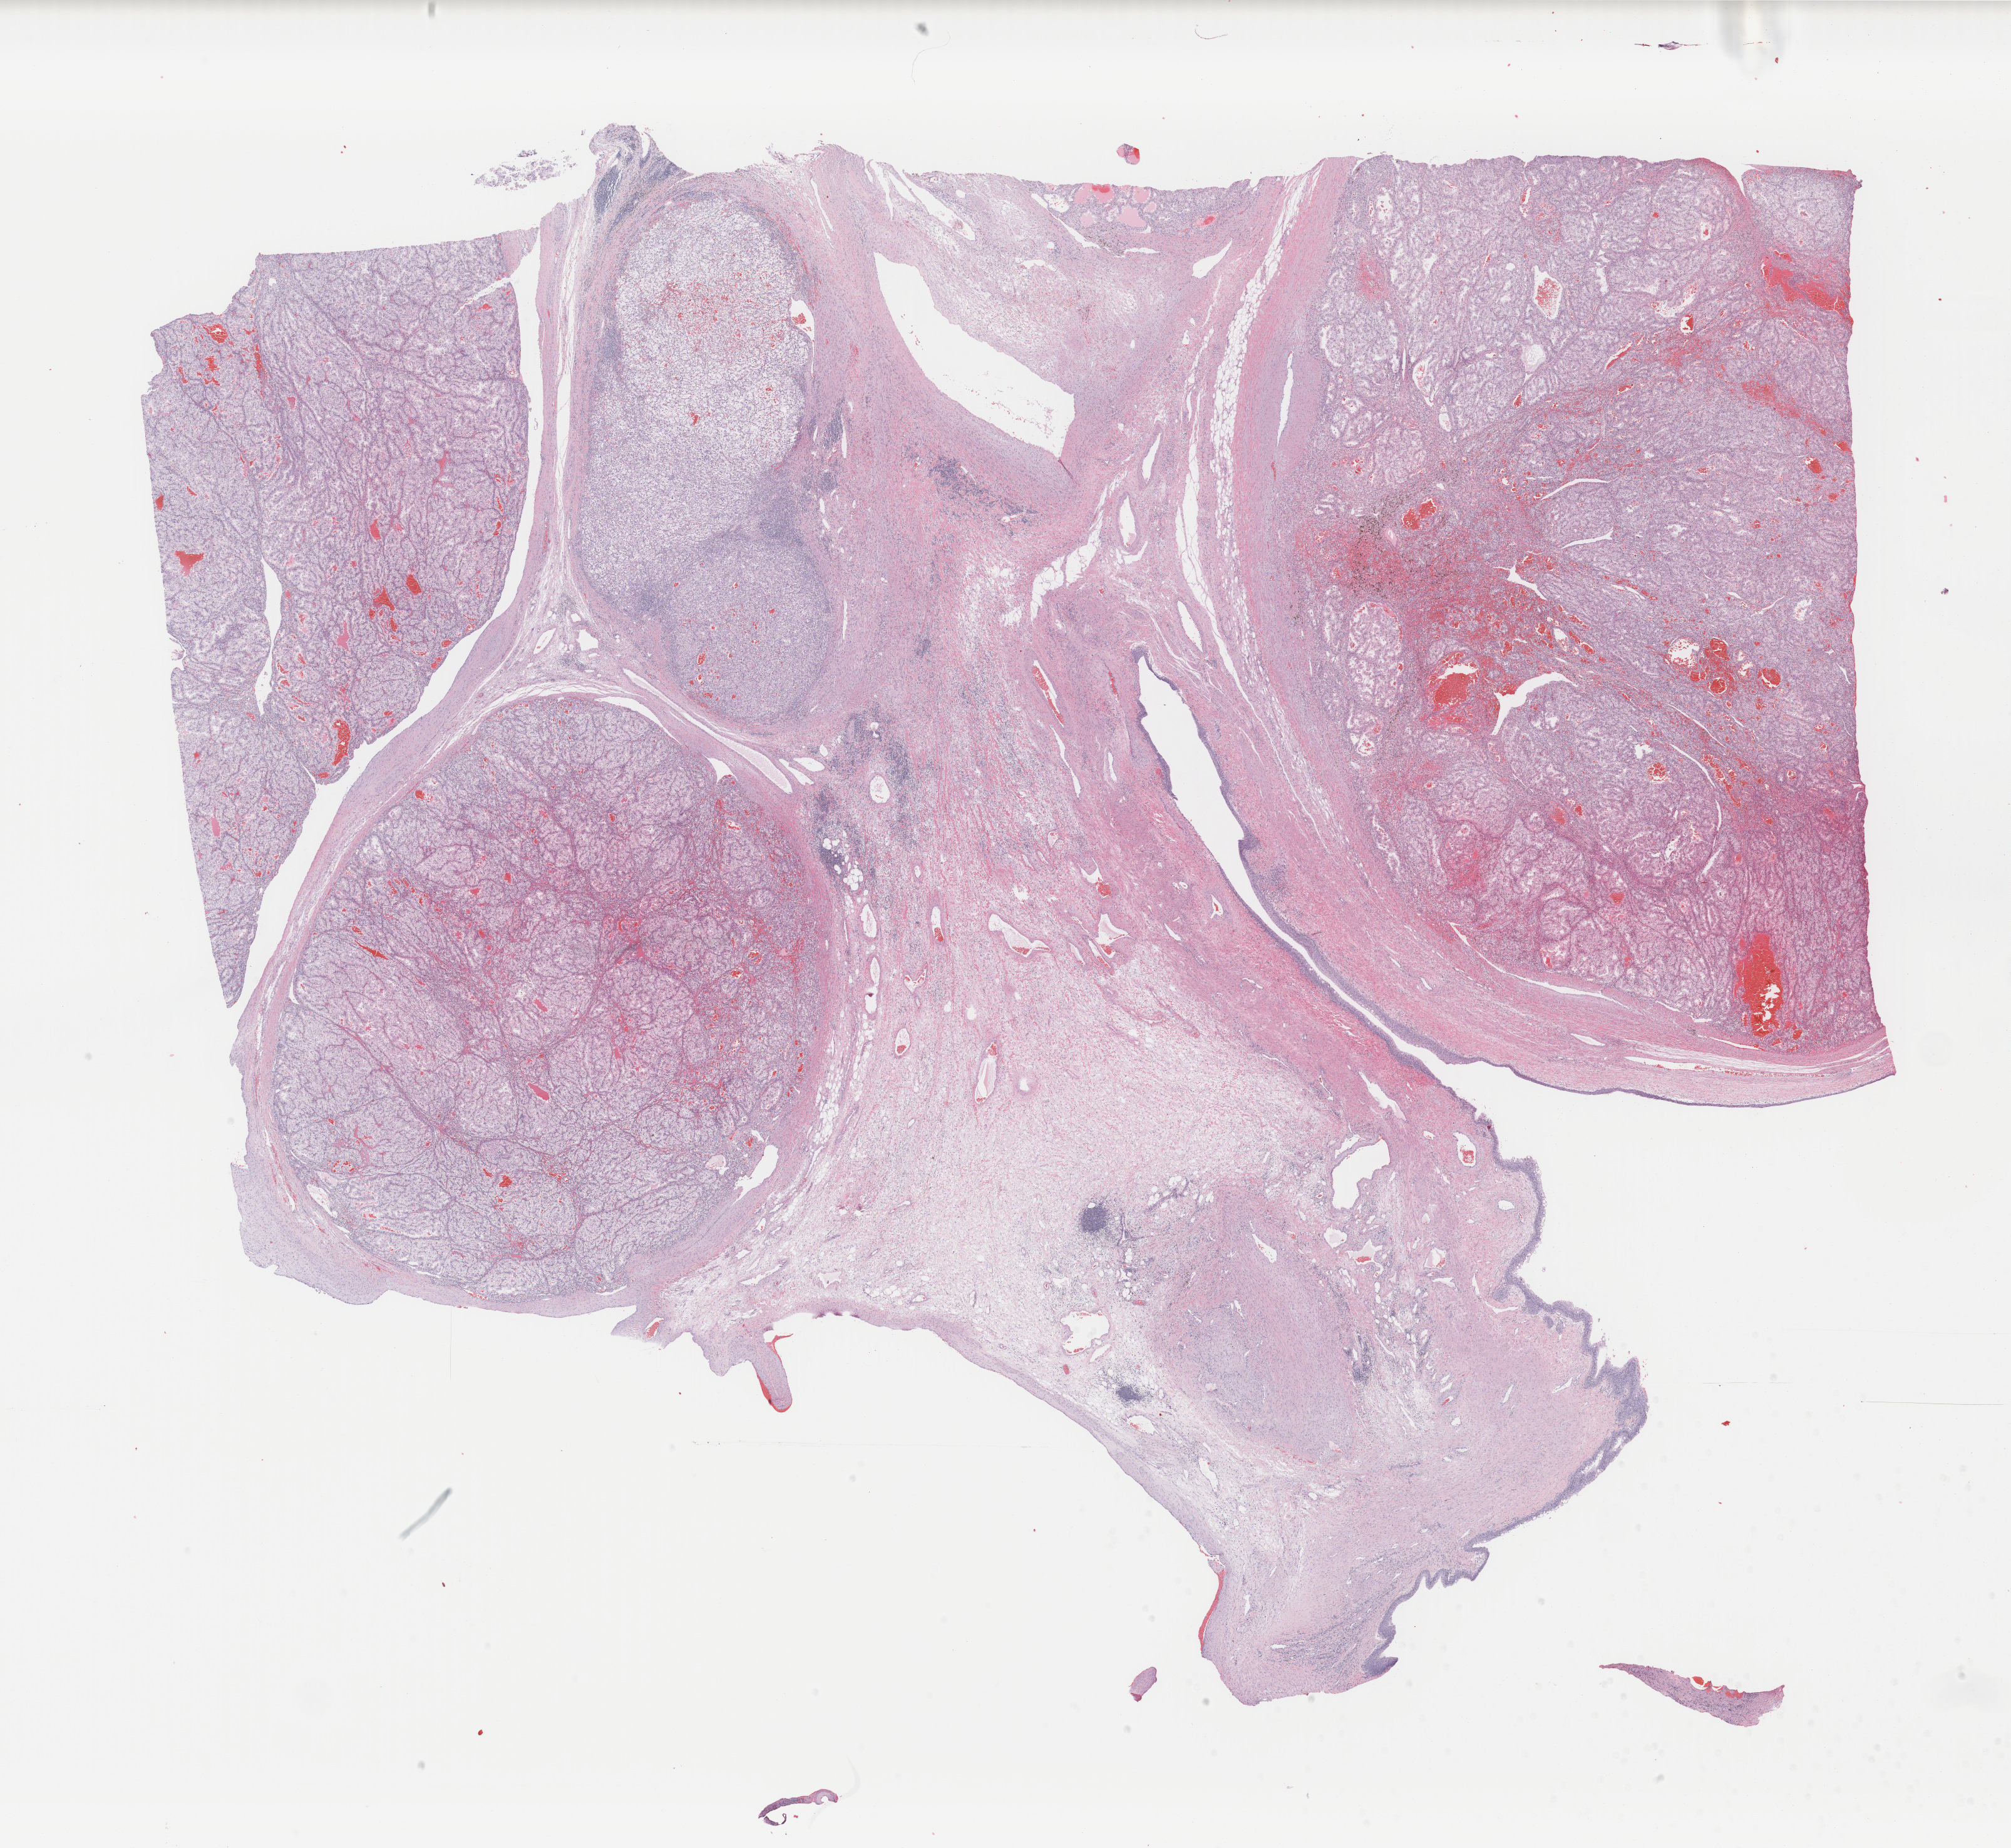
Digitized H&E tissue section (whole slide) — whole scanned area (about 25.5 x 23.4 mm, from a 40x scan) shown as a low-resolution overview; formalin-fixed paraffin-embedded (FFPE) diagnostic section; primary tumour sample from the kidney. Patient: female, age at initial diagnosis 54 years. Histologic grade: G4 (undifferentiated).
- laterality: left
- AJCC pathologic stage: IV (7th edition)
- histologic diagnosis: Clear cell adenocarcinoma, NOS
- TNM: T1b N0 M1
- lymph nodes positive (case pathology): 0 of 1 examined